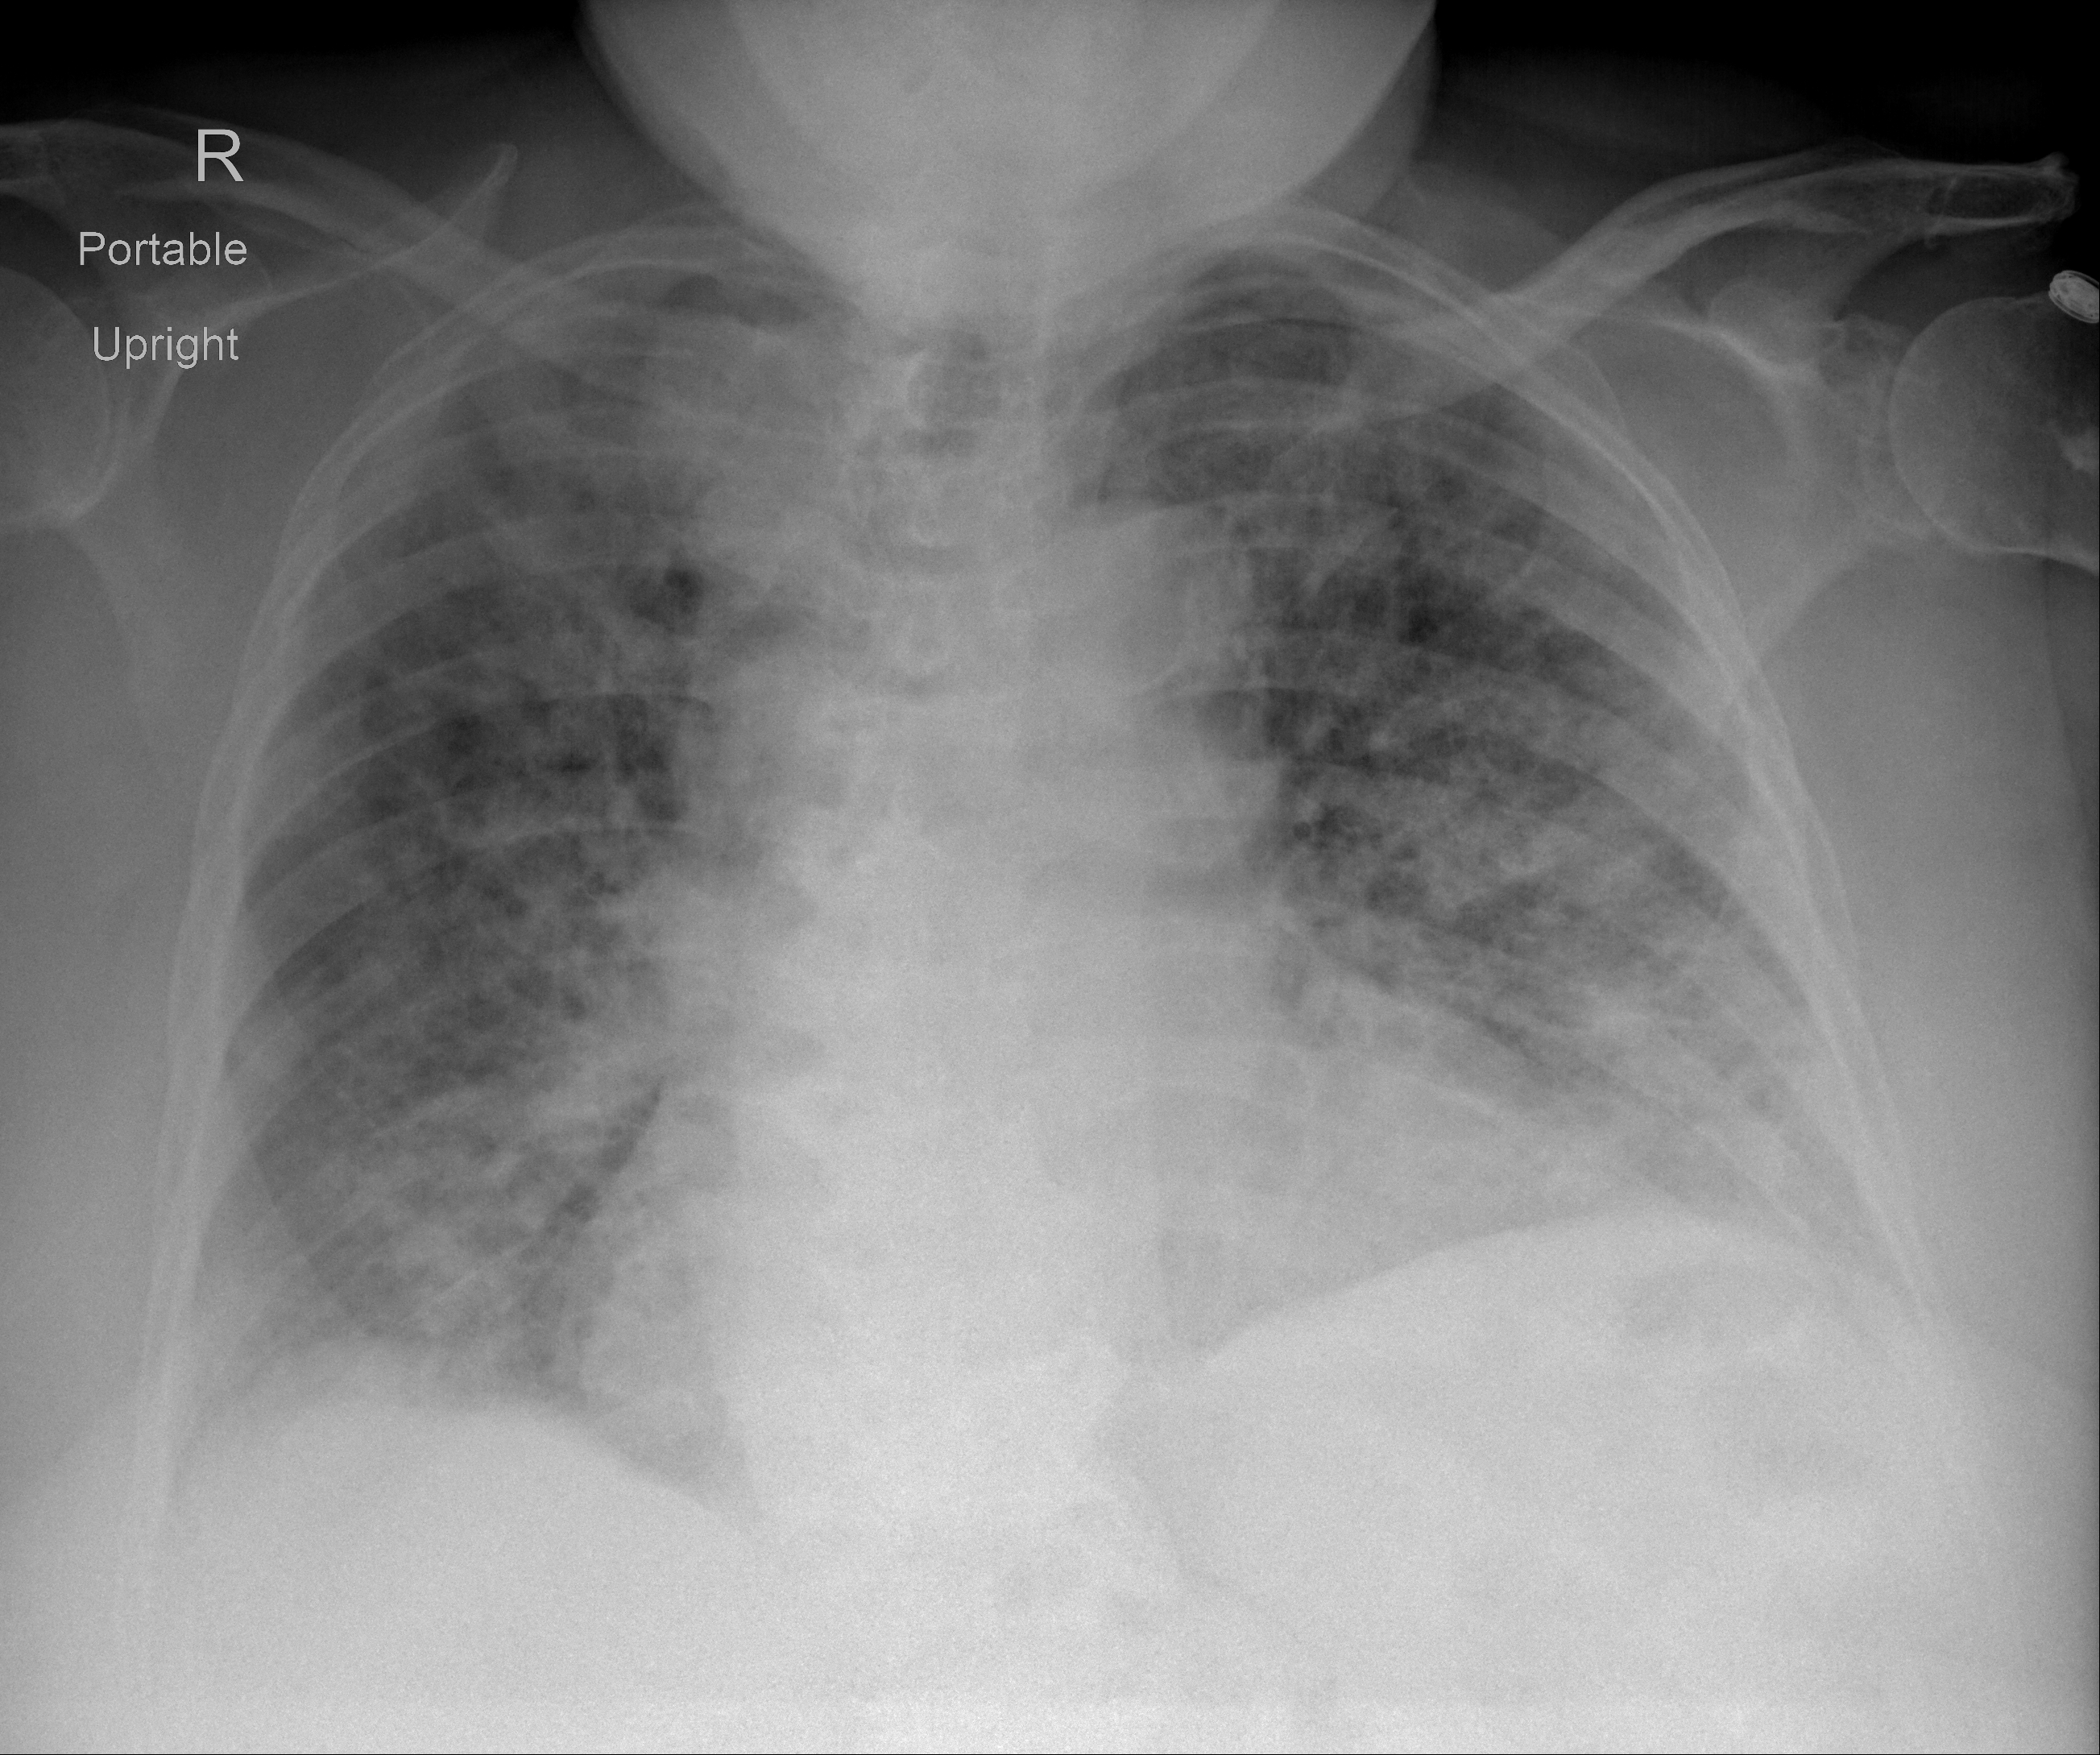
Portable chest radiograph, AP projection. Female patient, age 73 years; imaged 5 days after the COVID-19 diagnosis.
Key findings recorded by the radiologist: Diffuse opacities are again noted. There may be small layering pleural effusions.